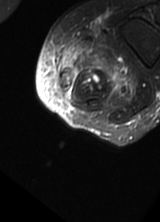
MRI of an extremity soft-tissue mass, one axial slice. Position 6 of 69 along the scan axis. T2-weighted fat-saturated. MR volume resampled by the dataset authors to the PET/CT grid (not the native acquisition matrix). 160 × 222 image matrix. Female patient. From the clinical record (not read from this slice): histological type: pleomorphic leiomyosarcoma; grade: high; site of the primary tumour: left thigh.
Structures marked on this image (expert contour drawn on MRI and transferred to this co-registered scan by the dataset authors):
- gross tumour volume including surrounding oedema: bounding box <55,34,137,99> (left, top, right, bottom; pixels)